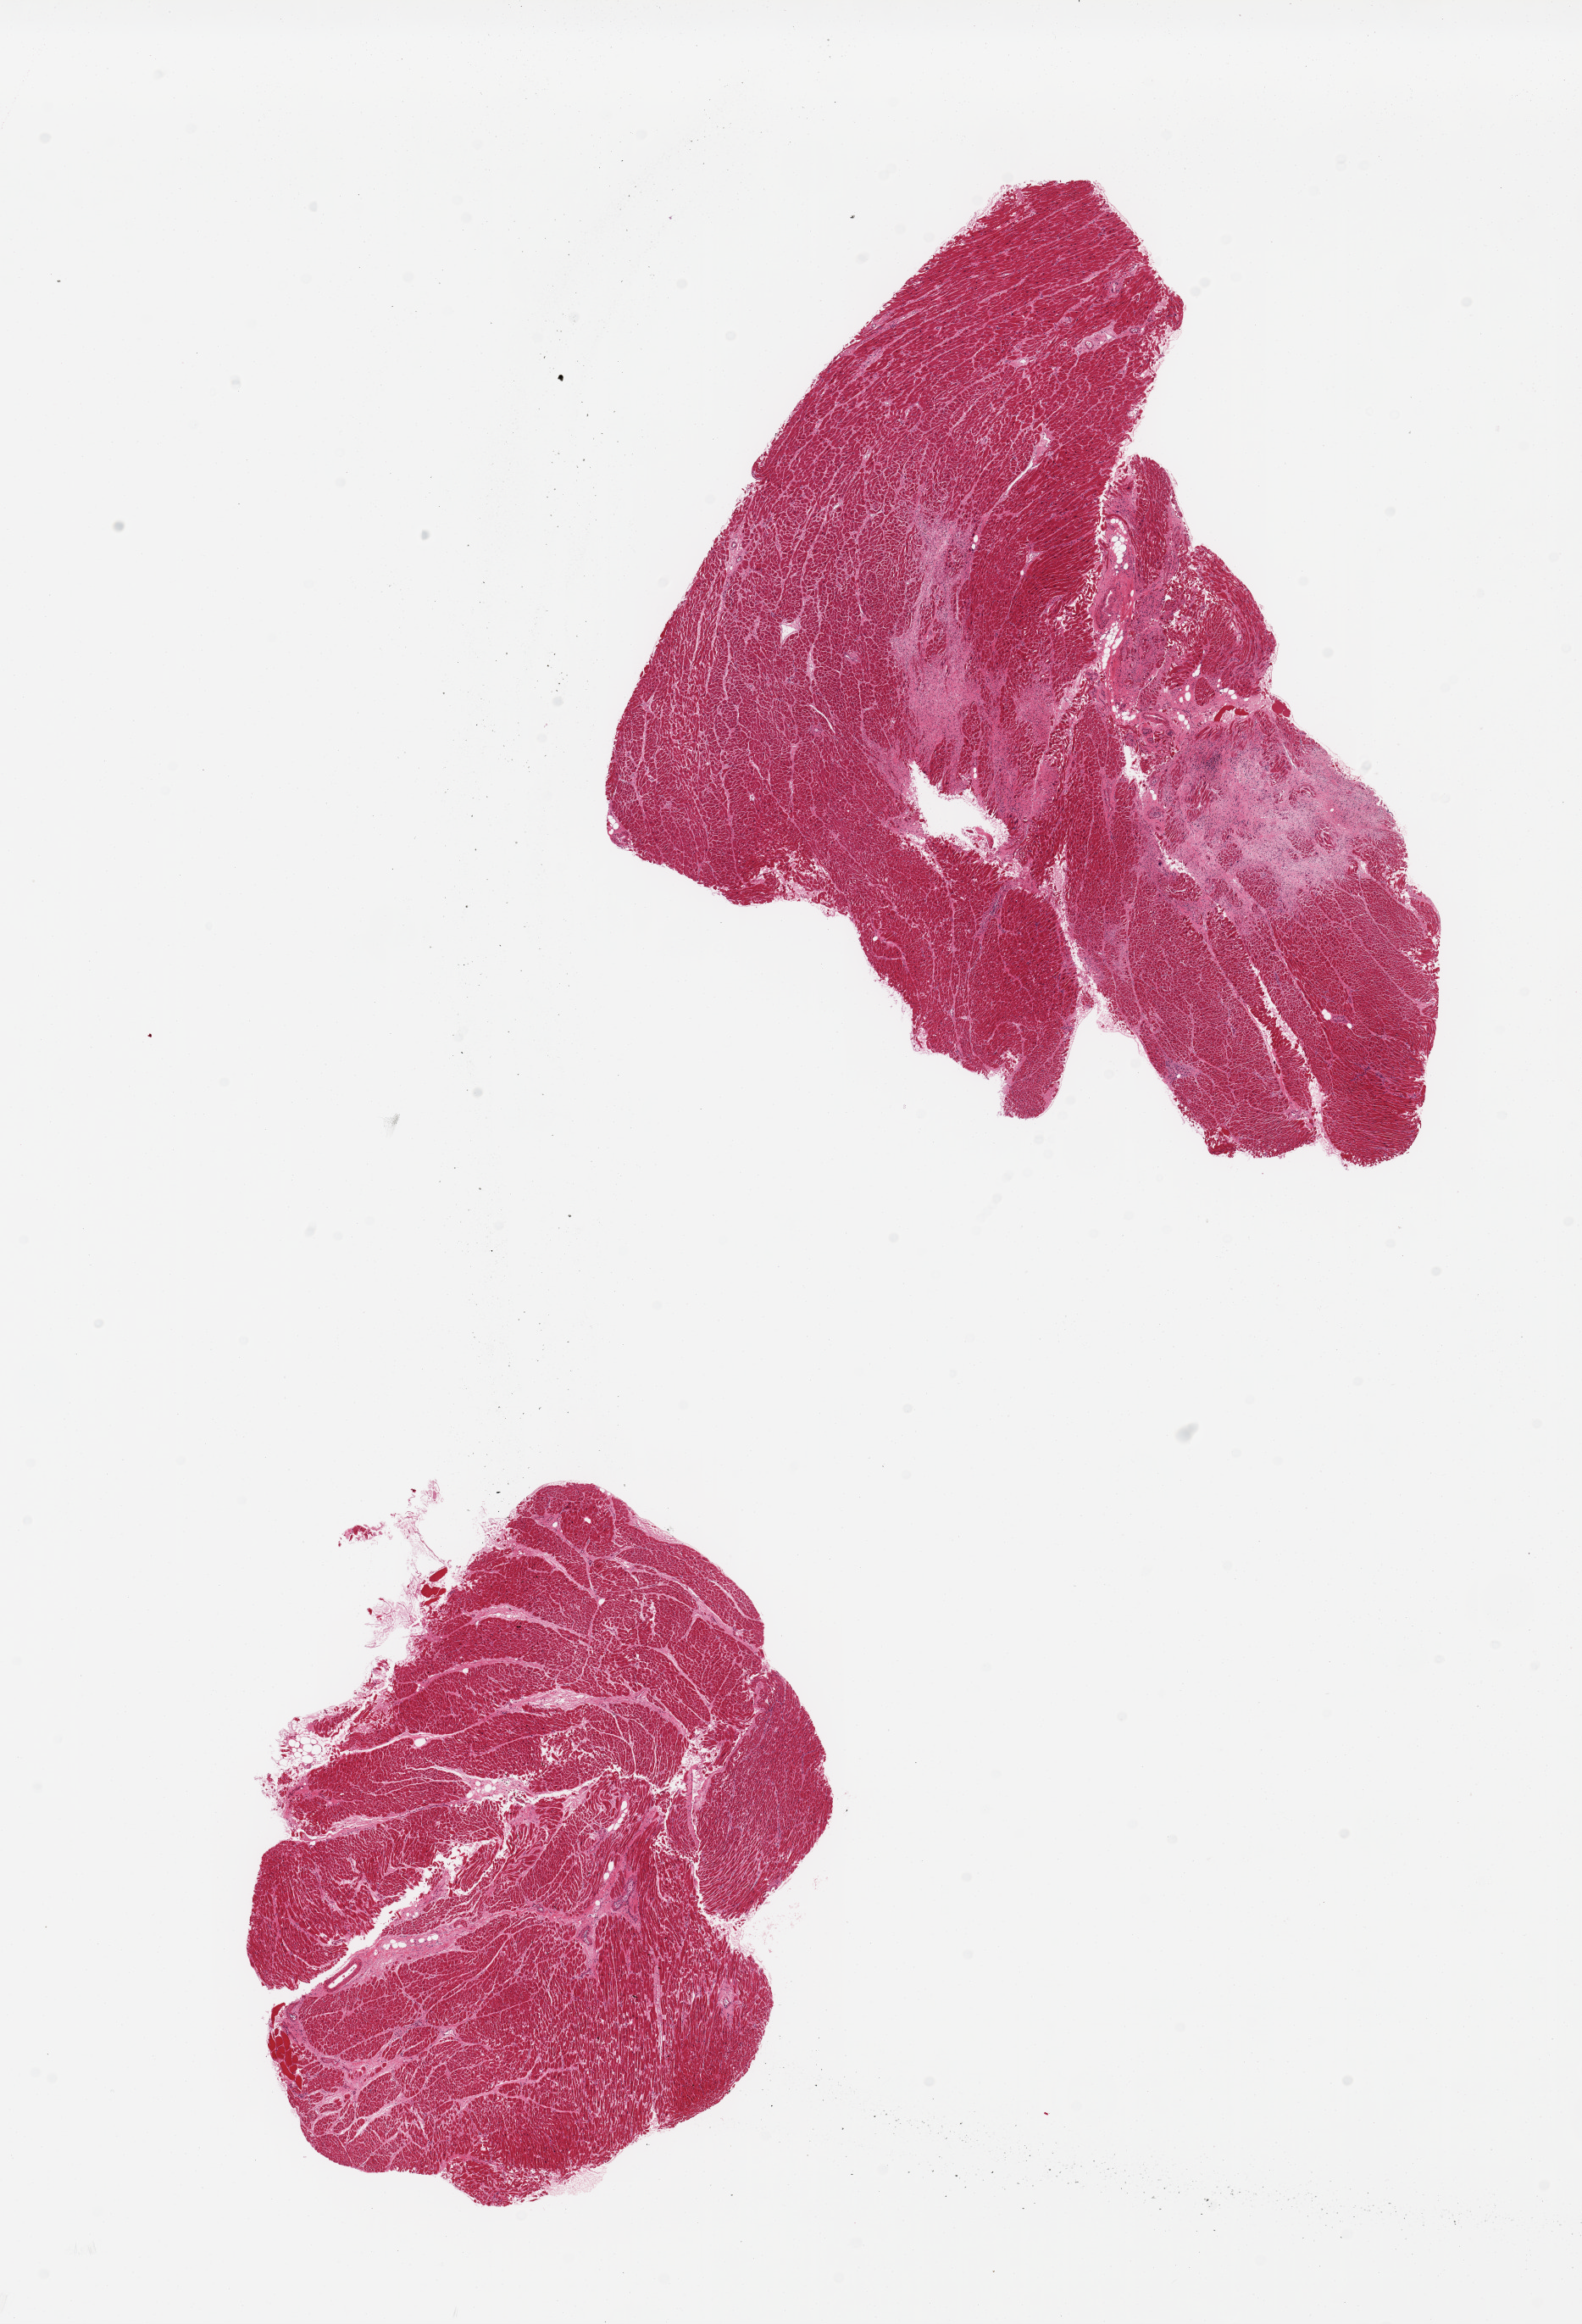
Whole-slide image, hematoxylin and eosin (H&E) stain, brightfield, shown as a low-resolution overview of the whole scanned area (about 14.8 x 21.7 mm, from a 20x scan); PAXgene-fixed, paraffin-embedded tissue; section of heart (target tissue); tissue donor sample. Male donor.
Reviewer comment on this tissue sample: 2 pieces, 1 with 15% scar tissue consistent with healed infarct.